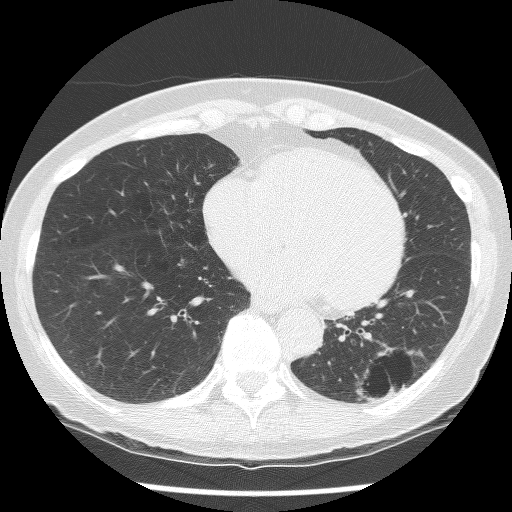
Chest CT (low-dose screening protocol), one axial image; second annual screen; lung window (W 1500 / L -600 HU); lung (sharp) reconstruction kernel (BONE); slice 86 of 136 in the series; 512 × 512 image matrix, field of view 300 × 300 mm. Female, age 61 years at enrolment. Current smoker at enrolment.
Lesion marked by an expert reader, box from (x=334, y=332) to (x=436, y=418) px. The screening reader recorded 2 non-calcified nodules or masses ≥4 mm on this exam (left lower lobe, left lower lobe); which of them this box marks is not recorded. Official screen result: positive, no significant change: stable abnormalities potentially related to lung cancer, unchanged since the prior screening exam. Later outcome: lung cancer diagnosed 585 days after this screen (after the third annual screen) — non-small cell carcinoma, left lower lobe, poorly differentiated (G3), stage IB (AJCC 6th edition), 100 mm at pathology.